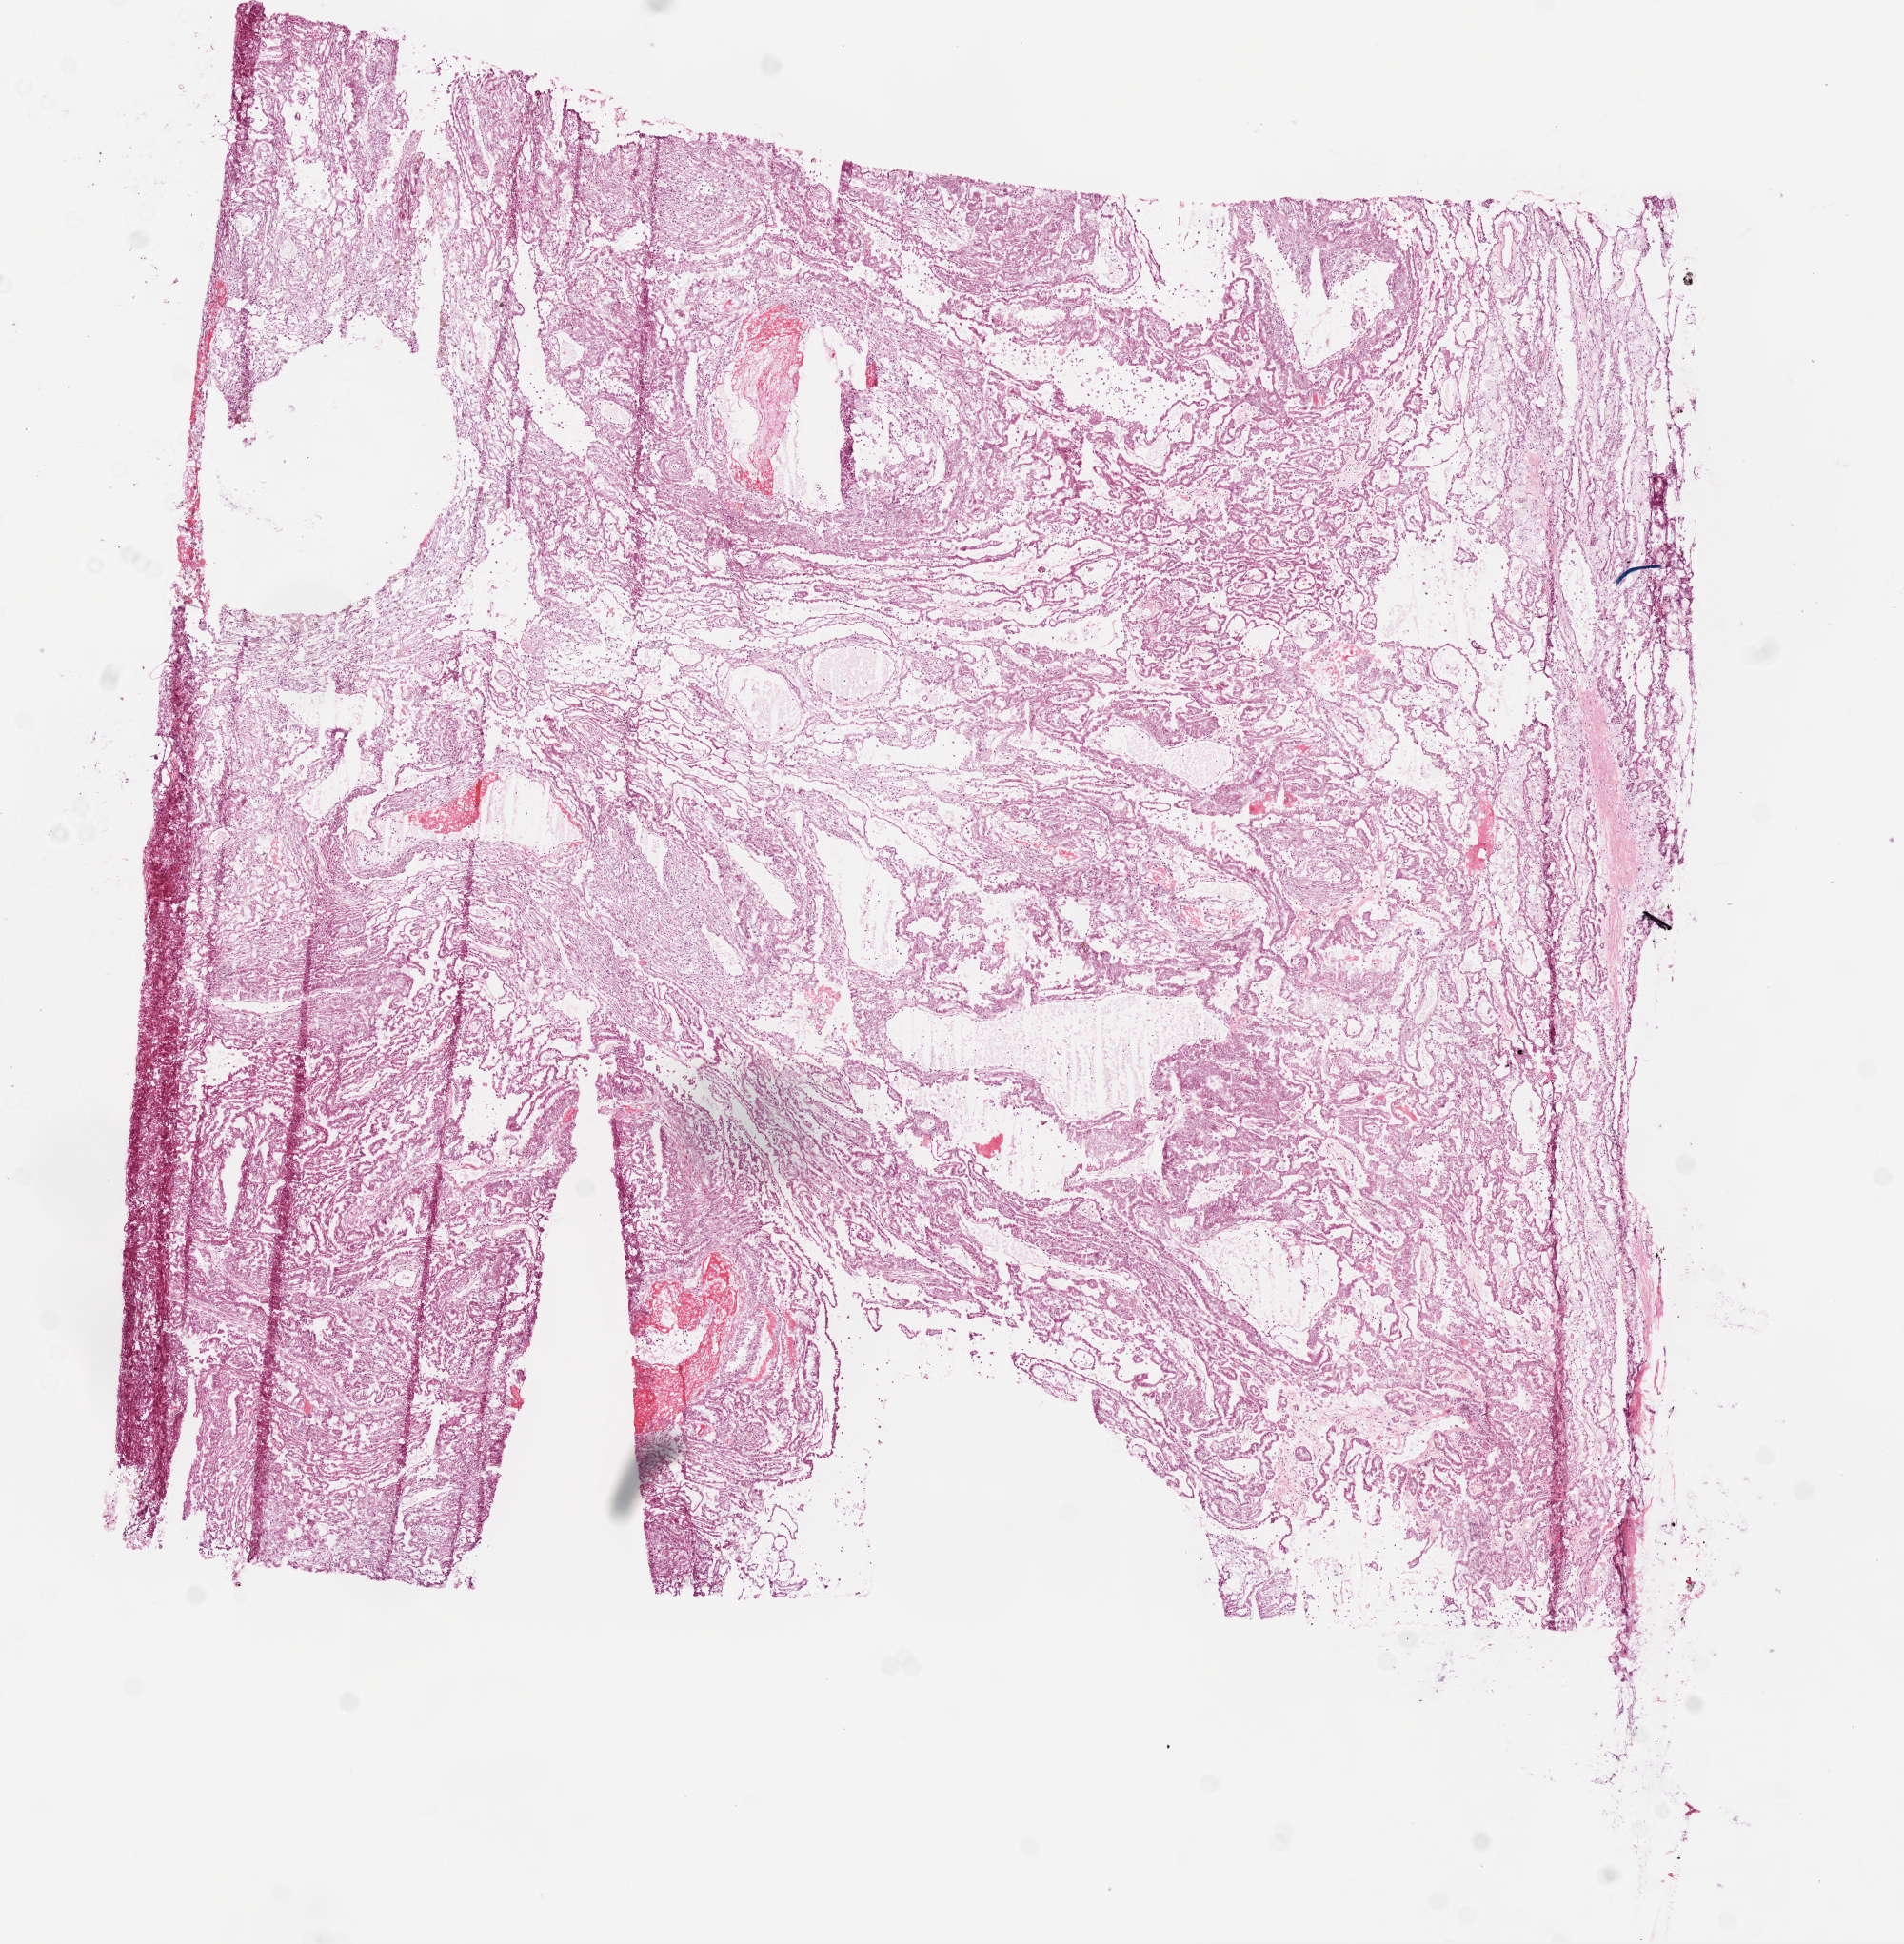
Digitized H&E-stained tissue section (whole slide), a low-resolution overview of the entire scanned area, about 8.0 x 8.2 mm (acquisition: 20x scan), frozen section, kidney, primary tumour sample. Male, age 63 years at initial diagnosis. Histologic grade: G3 (poorly differentiated). Pathologist review of this section (percent, as recorded): tumour cells 90%, tumour nuclei 80%, normal cells 0%, stromal cells 10%, necrosis 0%.
- AJCC pathologic stage: I (7th edition)
- pathologic diagnosis: Clear cell adenocarcinoma, NOS
- laterality: left